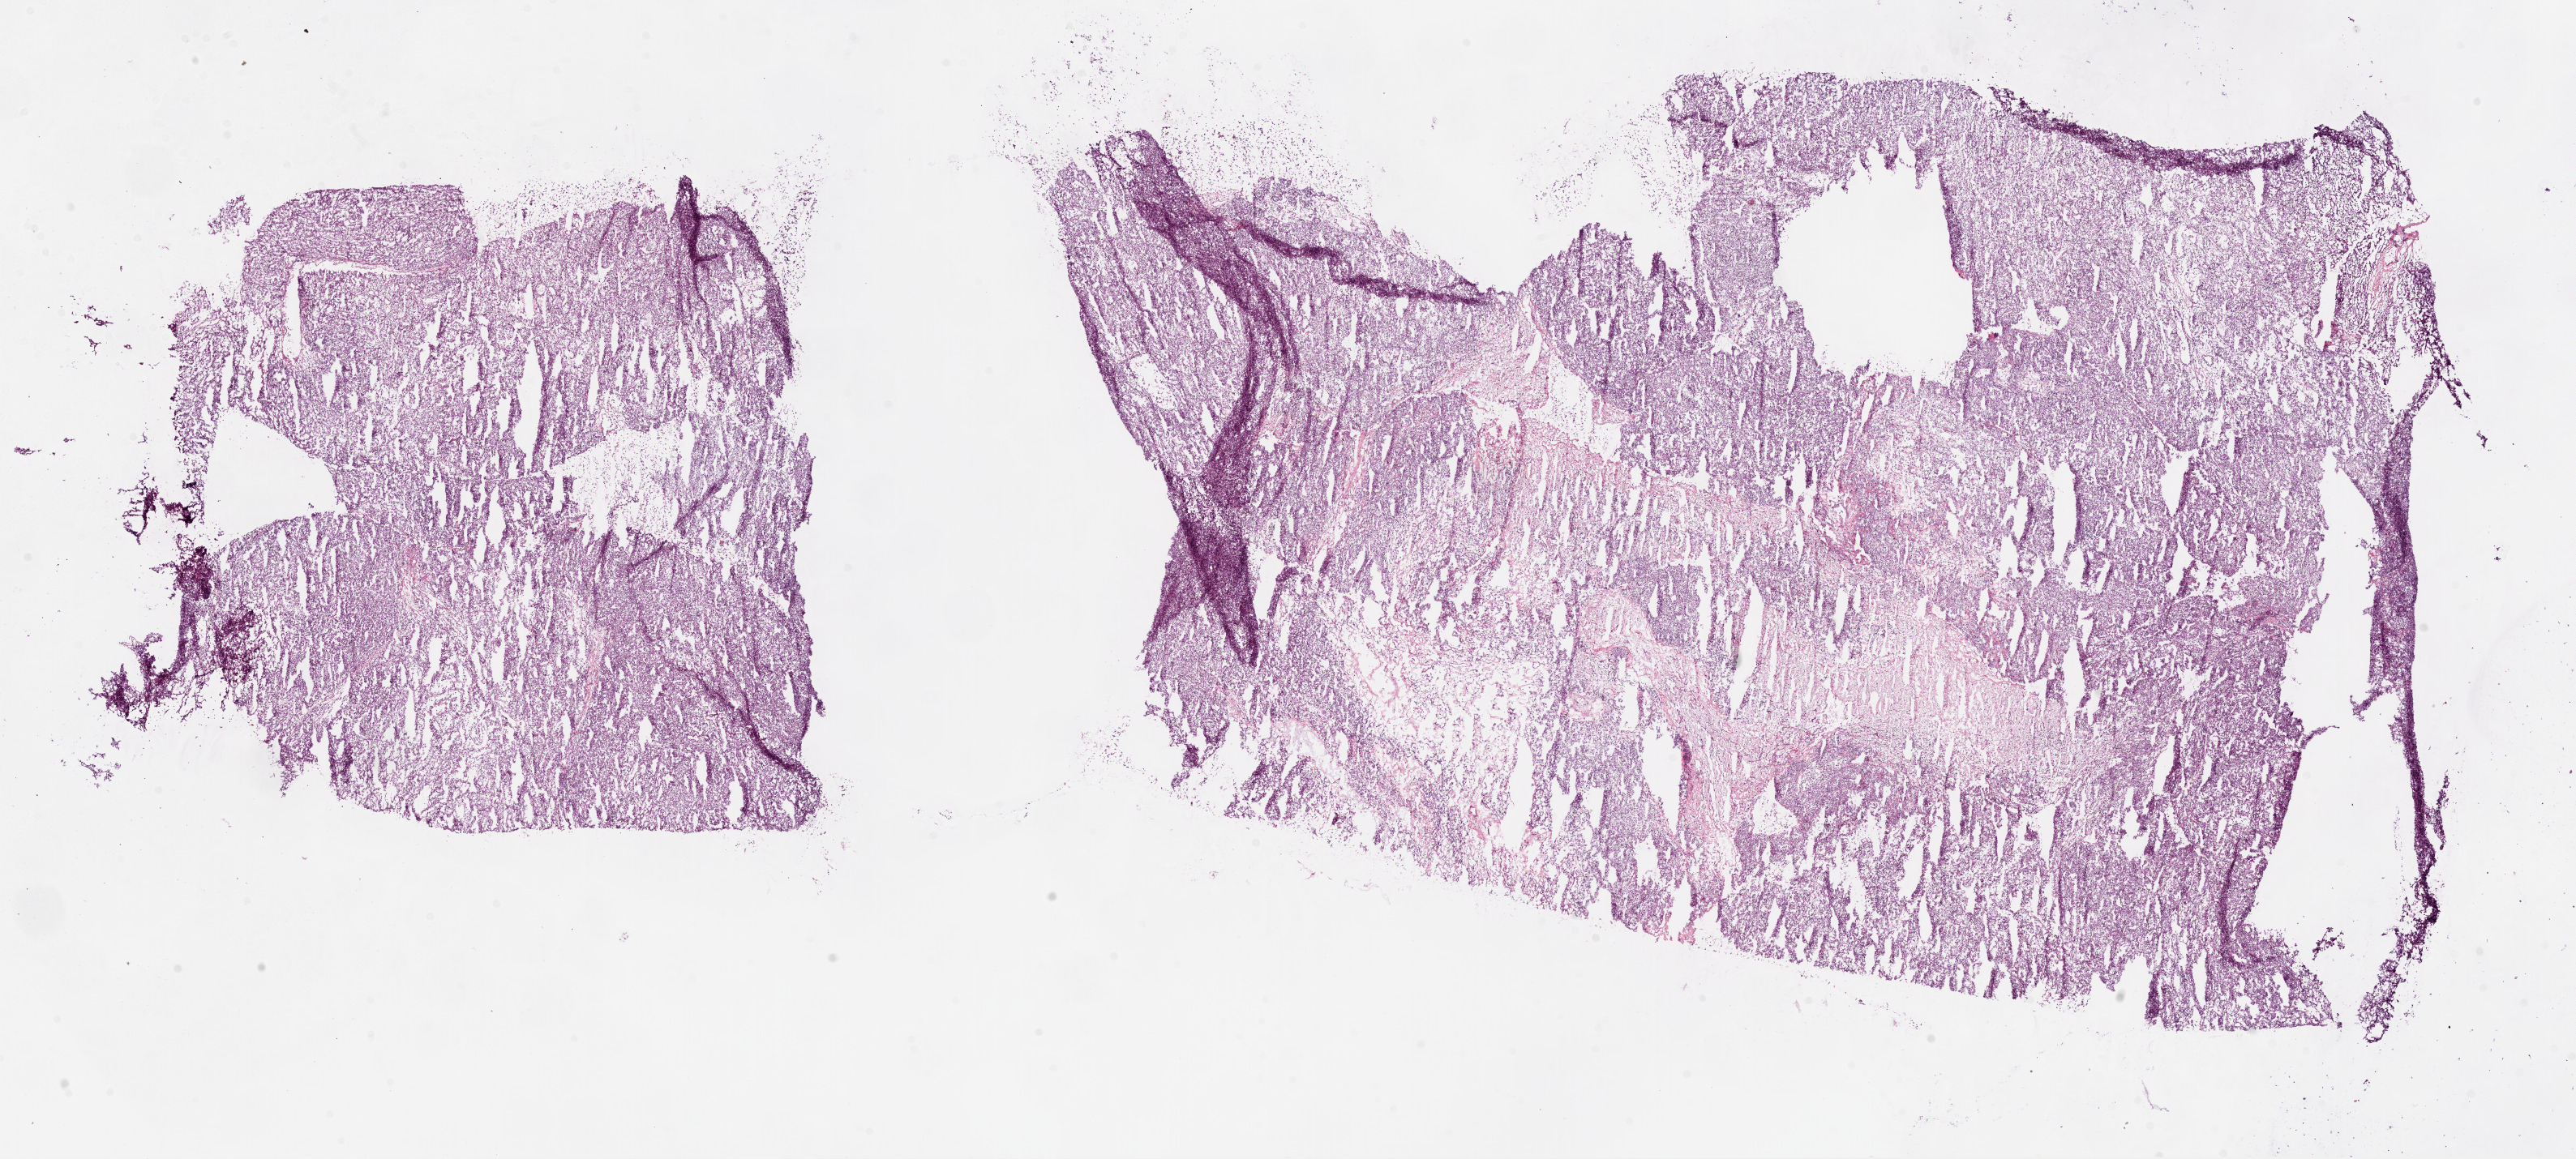
Whole-slide histology image, Hematoxylin and eosin (H&E) stained, a low-resolution overview of the entire scanned area, about 25.6 x 11.5 mm (from a 20x scan). Frozen section from the bottom of the tissue portion. Sample: primary tumour, kidney. Male patient; age at initial diagnosis 70 years. Histologic grade: G3 (poorly differentiated). Composition of this section per pathologist review: tumour cells 88%, tumour nuclei 85%, normal cells 0%, stromal cells 12%, necrosis 0%.
- laterality: right
- histologic diagnosis: Clear cell adenocarcinoma, NOS
- AJCC pathologic stage: II (7th edition)
- TNM: T2a NX M0